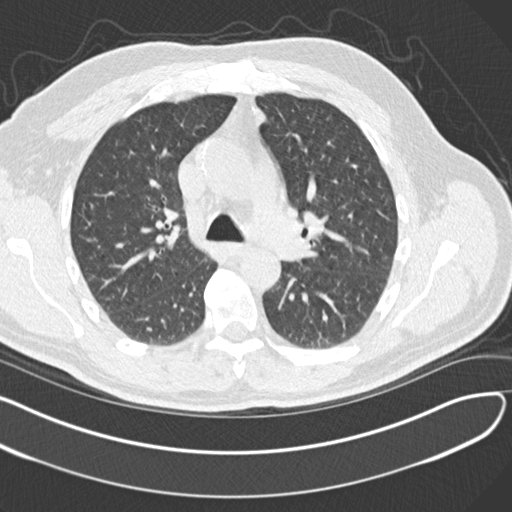
Chest CT (low-dose screening protocol), one axial image. Second screening round (one year after baseline). Lung window (W 1500 / L -600 HU). 120 kVp. 512 × 512 image matrix, field of view 372 × 372 mm. Male participant, aged 65 years at enrolment.
Lesion marked by an expert reader, bounding box <289,194,354,260> (left, top, right, bottom; pixels). The screening reader recorded 4 non-calcified nodules or masses ≥4 mm on this exam (left upper lobe, left upper lobe, left lower lobe, right middle lobe); which of them this box marks is not recorded. Official screen result: positive, other.